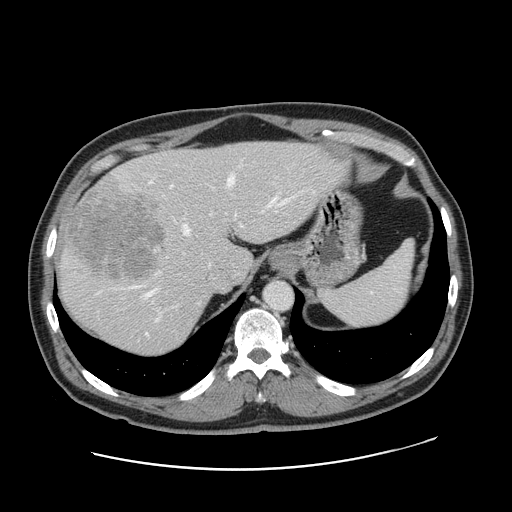
Contrast-enhanced abdominal CT, one axial slice. Position 123 of 178 along the scan axis. 120 kVp. Soft-tissue window (W 400 / L 40 HU). 2.5 mm slice thickness. 512 × 512 image matrix, field of view 403 × 403 mm. Male patient, age 63 years. Case-level facts recorded for this patient, not image findings: diagnosis: colorectal cancer liver metastases, imaged before liver resection; multiple liver metastases: yes; largest metastasis: 8 cm; disease in both lobes: yes.
Annotated regions visible in this slice (expert manual segmentation):
- hepatic veins: box from (x=133, y=175) to (x=276, y=296) px
- liver: (x=59, y=142)–(x=344, y=356)
- planned liver remnant (the part of the liver to remain after resection): (x=145, y=142)–(x=344, y=281)
- portal vein (with intrahepatic branches): (x=154, y=185)–(x=244, y=321)
- liver metastasis: (x=66, y=181)–(x=165, y=280)